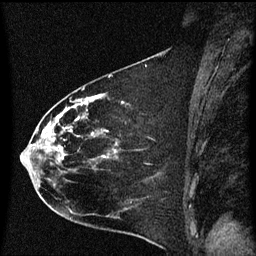
Breast MRI (dynamic contrast-enhanced), one sagittal slice. Position 31 of 60 along the scan axis. Dynamic contrast-enhanced series, image 2 of 3 at this slice position (ordered by acquisition). 1.5 T. TE 4.2 ms, TR 8.4 ms. 2 mm slice thickness. 256 × 256 image matrix, field of view 200 × 200 mm. Patient: female, 35 years. From the clinical record (not read from this slice): setting: breast cancer imaged before/during neoadjuvant chemotherapy; receptor status: HER2-positive.
Outlined on this slice (semi-automatic segmentation, software-assisted and operator-edited):
- analysis volume of interest (the breast-tissue region the enhancement analysis was run in; not a lesion): bounding box [x1, y1, x2, y2] px = [22, 68, 174, 173]
- tumour enhancement mask (voxels above the 70 % enhancement threshold inside the analysis volume of interest): [34, 96, 106, 161]